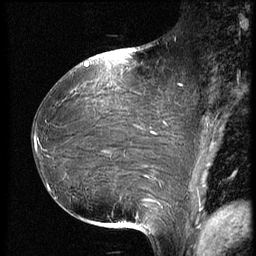
Breast MRI (dynamic contrast-enhanced), one sagittal slice; slice 34 of 66 in the series (ordered by position); dynamic contrast-enhanced series, image 2 of 3 at this slice position (ordered by acquisition); 1.5 T; TE 4.2 ms, TR 8.9 ms; 2.5 mm slice thickness; 256 × 256 image matrix, field of view 200 × 200 mm. Patient: female, 39 years. From the clinical record (not read from this slice): setting: breast cancer imaged before/during neoadjuvant chemotherapy; receptor status: HER2-positive.
Annotated regions visible in this slice (semi-automatic segmentation, software-assisted and operator-edited):
- analysis volume of interest (the breast-tissue region the enhancement analysis was run in; not a lesion): bounding box <32,75,188,218> (left, top, right, bottom; pixels)
- tumour enhancement mask (voxels above the 140 % enhancement threshold inside the analysis volume of interest): <35,136,145,201>